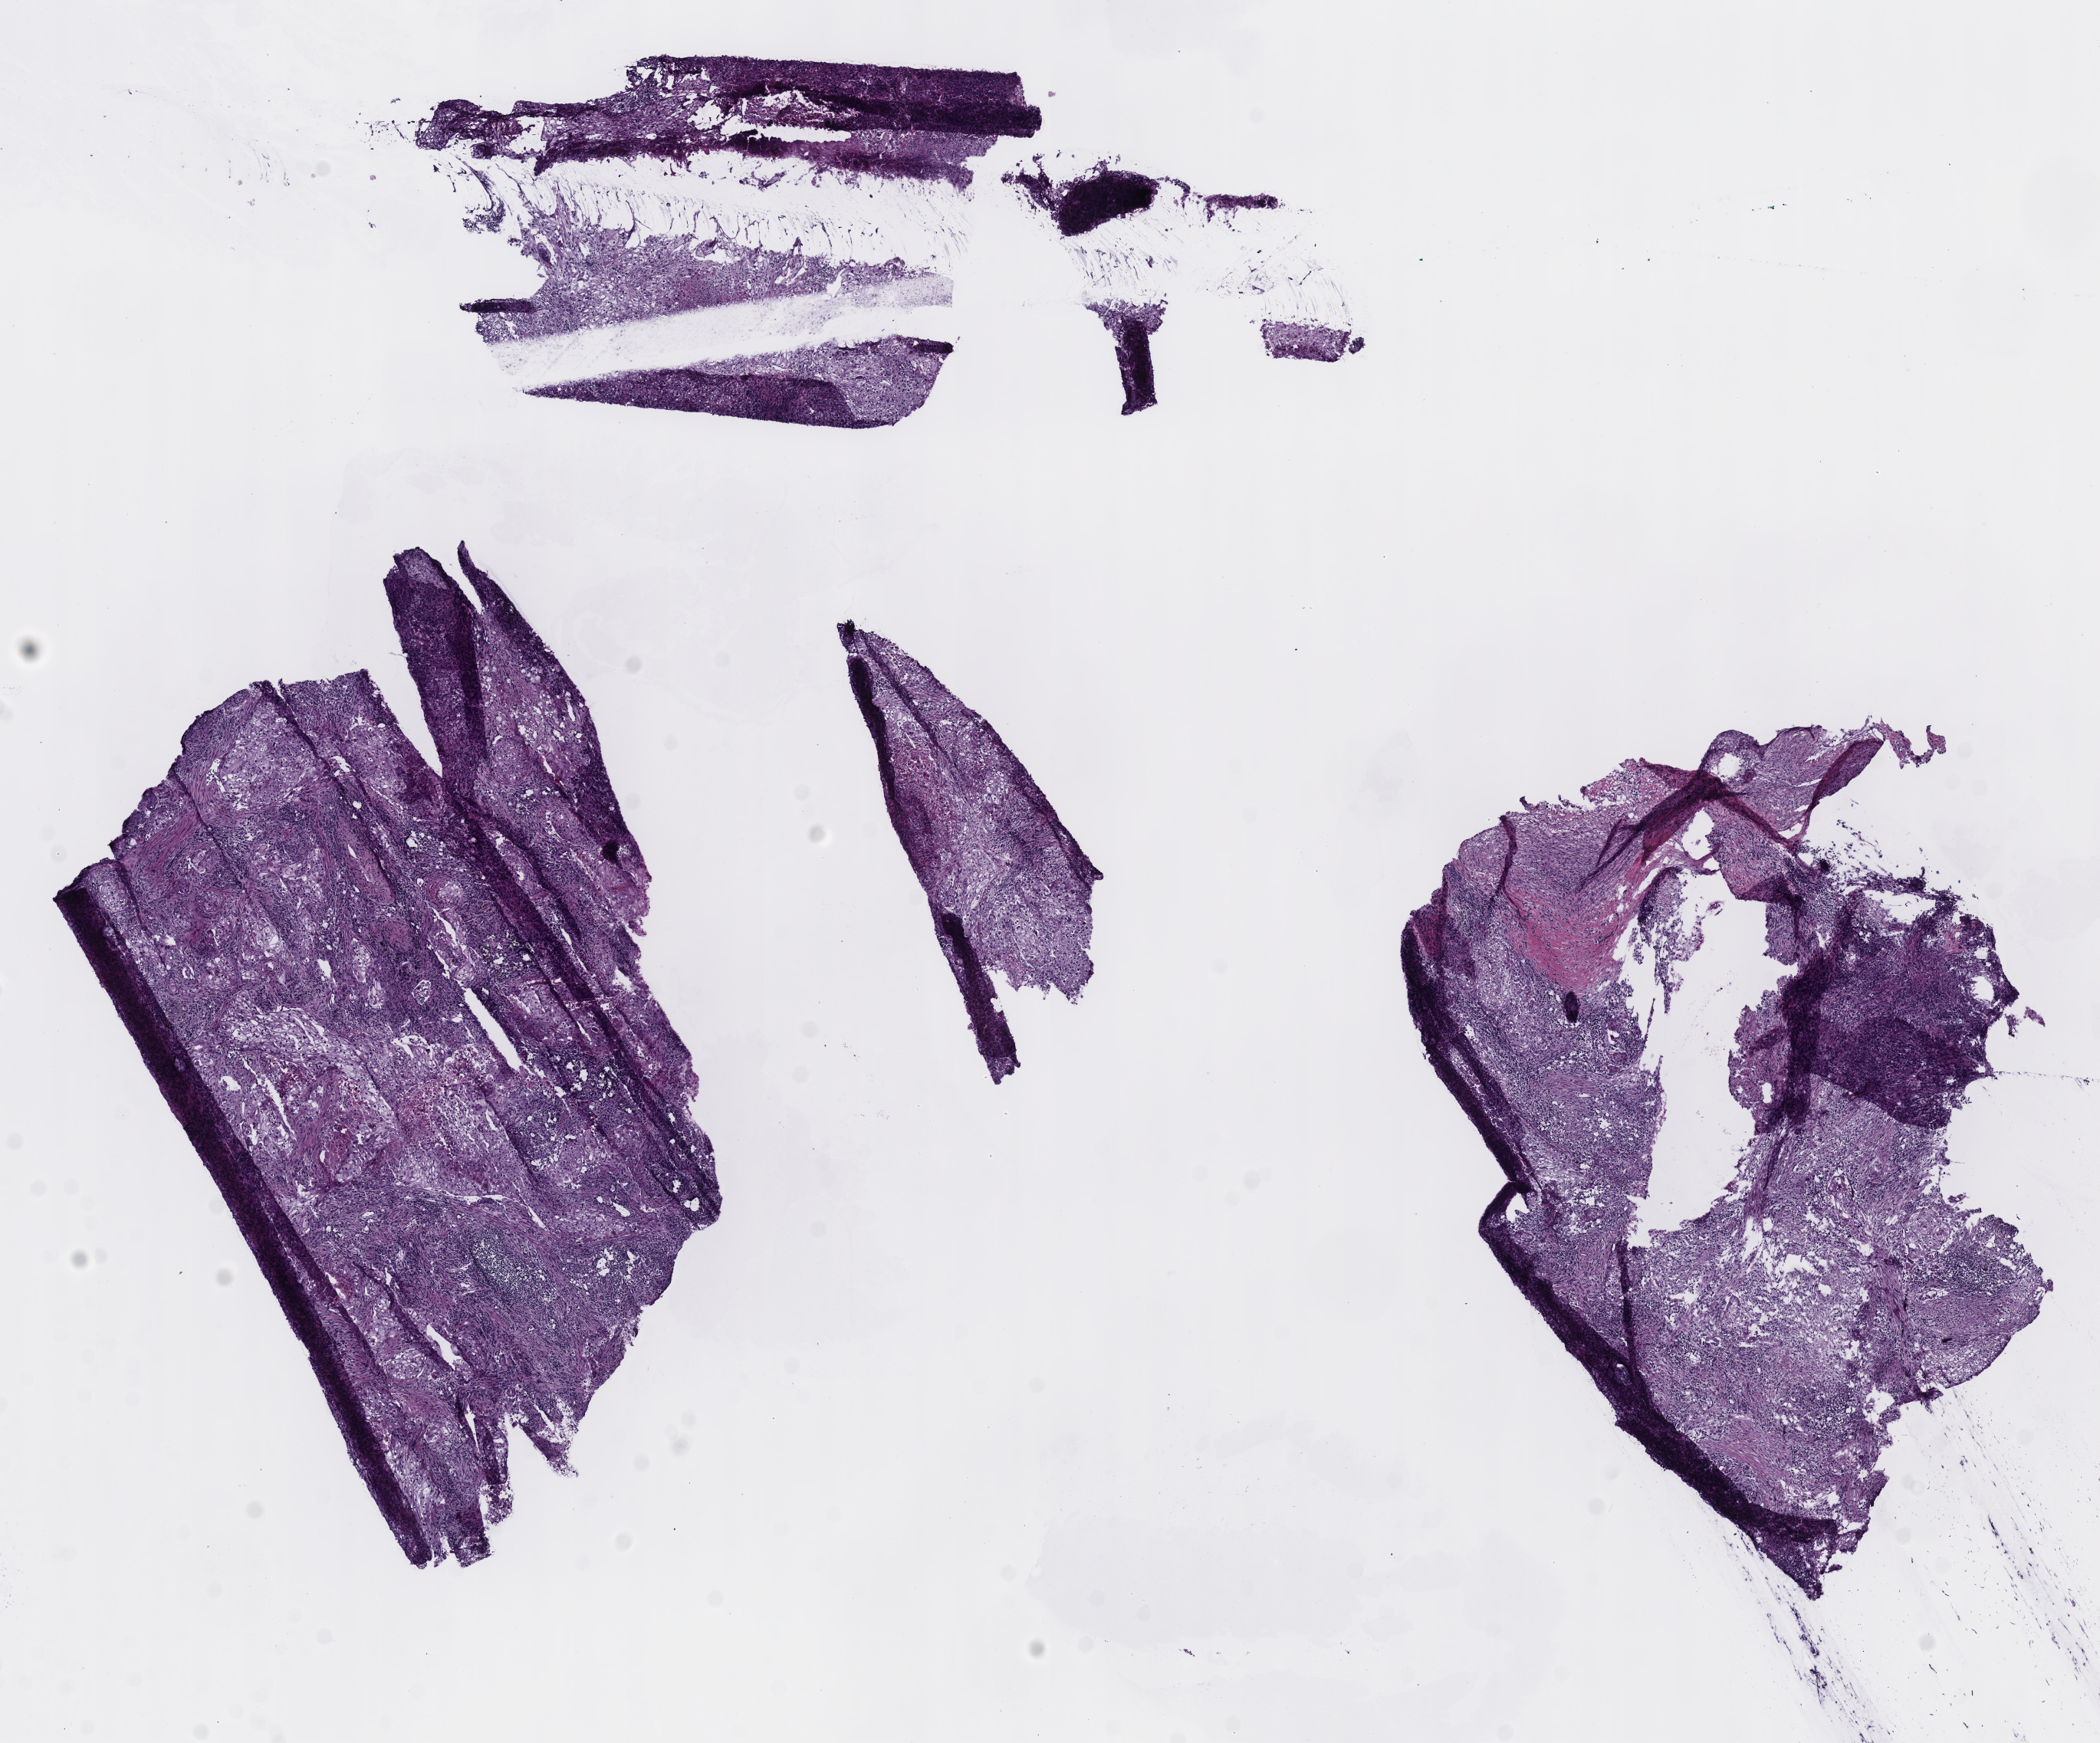
Whole-slide histology image, Hematoxylin and eosin (H&E) stained — low-resolution overview of the scanned area, about 10.8 x 8.9 mm (from a 40x scan), frozen section from the top of the tissue portion, sample: solid tissue normal (non-tumour tissue), lung. Male, age 64 years at initial diagnosis.
This section: solid tissue normal sample (biorepository sample class). Patient diagnosis: Squamous cell carcinoma, NOS.